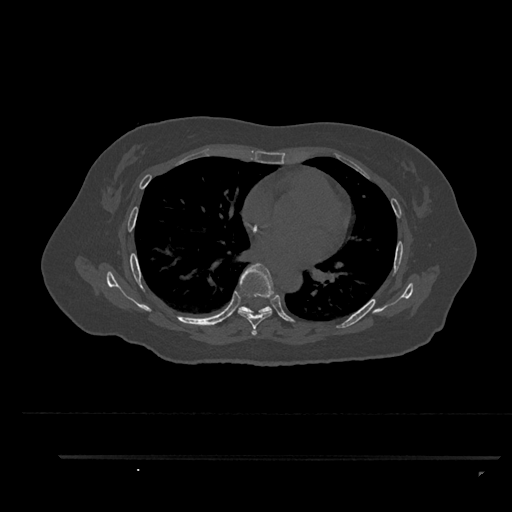
CT including the spine, one axial slice; slice 539 of 797 in the series (ordered by position); reconstruction kernel Br40s/3; bone window (W 1800 / L 400 HU); 0.5 mm slice thickness; 512 × 512 image matrix. Patient: female, 44 years. Case-level facts recorded for this patient, not image findings: primary cancer: renal; vertebrae with lytic lesions (as recorded): L1.
Annotated regions visible in this slice (semi-automatic segmentation, software-assisted and operator-edited):
- T6 vertebra: bounding box [x1, y1, x2, y2] px = [238, 263, 275, 336]
- T7 vertebra: [238, 306, 273, 315]